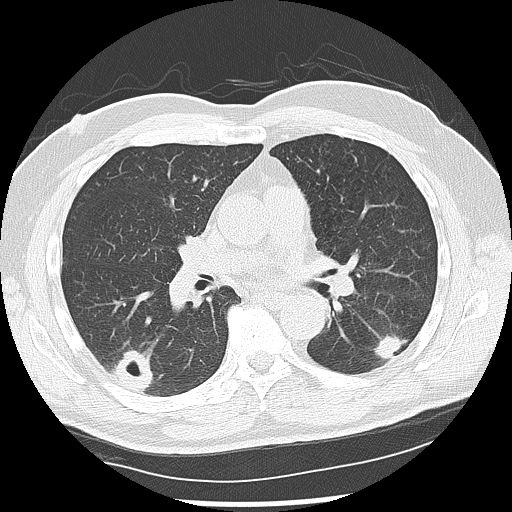
Low-dose screening chest CT, one axial slice; slice 71 of 142 in the series (ordered by position); 120 kVp; lung window (W 1500 / L -600 HU); 2.5 mm slice thickness; 512 × 512 image matrix, field of view 360 × 360 mm.
Outlined on this slice (outlined manually by an expert reader):
- lesion 1 (nodule, lower lobe of left lung): bounding box <373,335,408,364> (left, top, right, bottom; pixels)
- lesion 2 (nodule, lower lobe of right lung): <110,349,154,392>